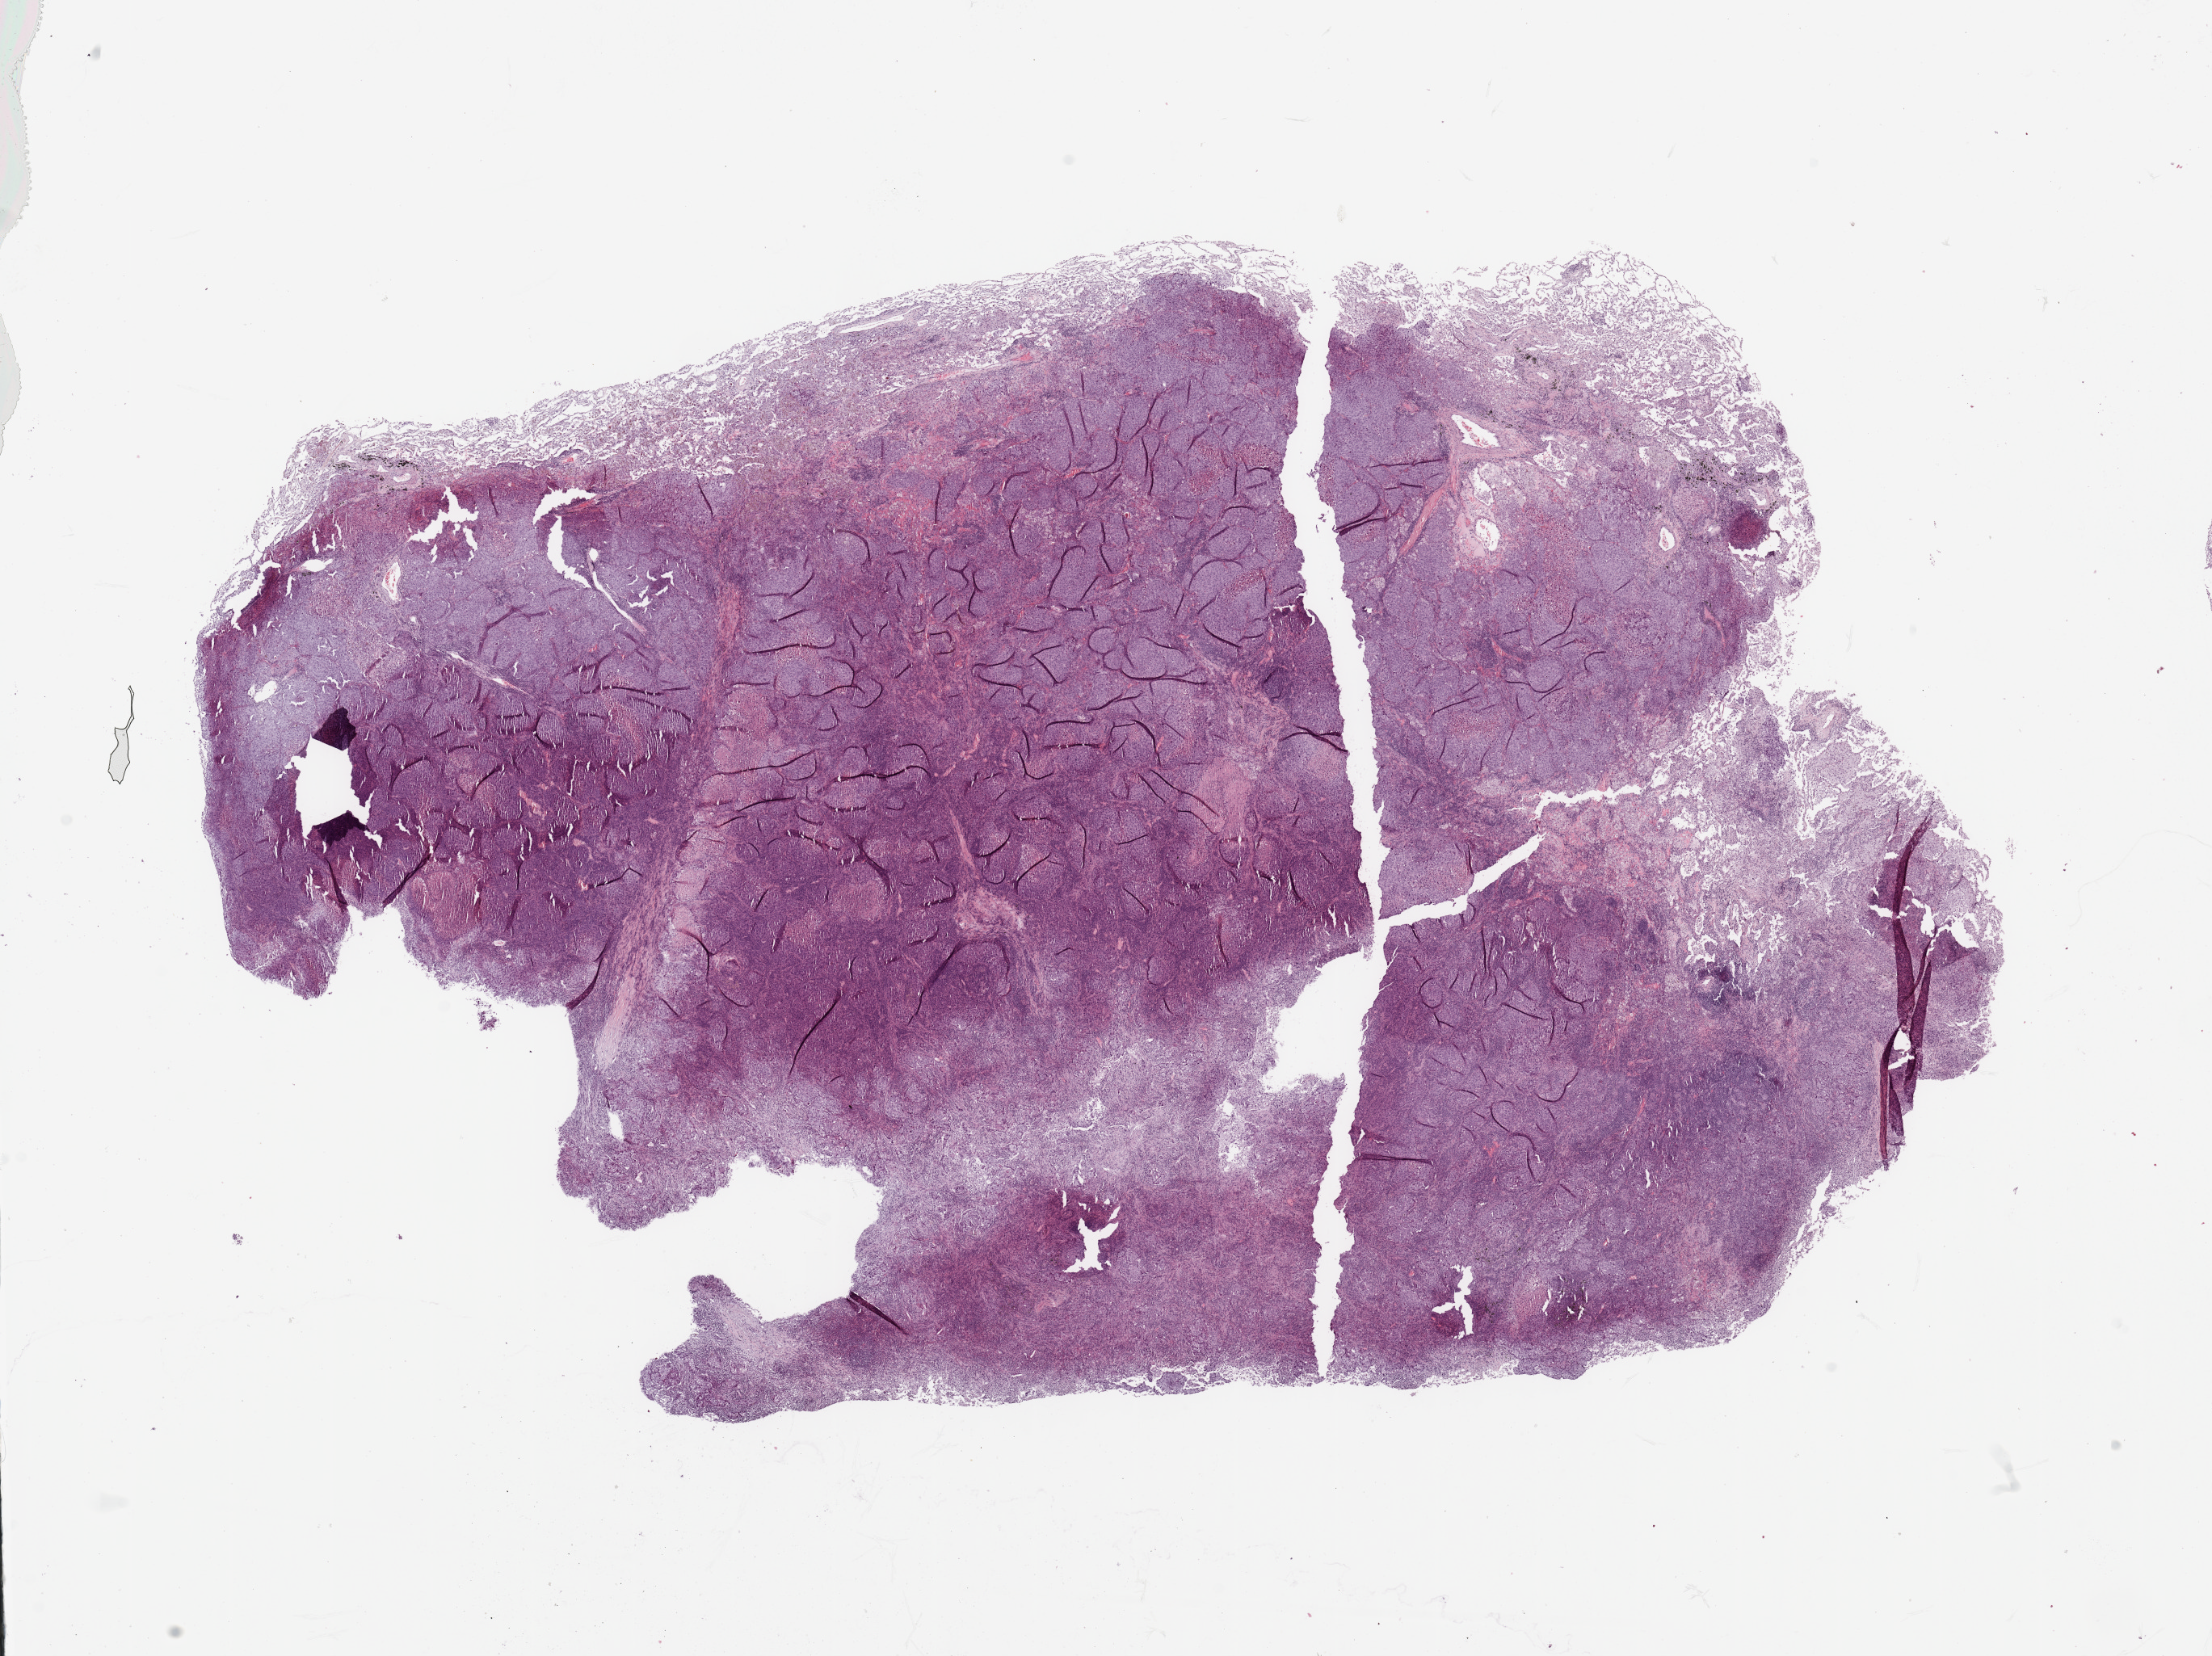
Hematoxylin and eosin (H&E) stained whole-slide image, shown as a low-resolution overview of the whole scanned area (about 21.7 x 16.2 mm, slide scanned at 20x). Lung, tumour tissue. Male, 61 y/o. Histologic grade: G2 (moderately differentiated).
• primary tumour site (as recorded): right upper lobe
• histologic diagnosis: Squamous cell carcinoma, NOS